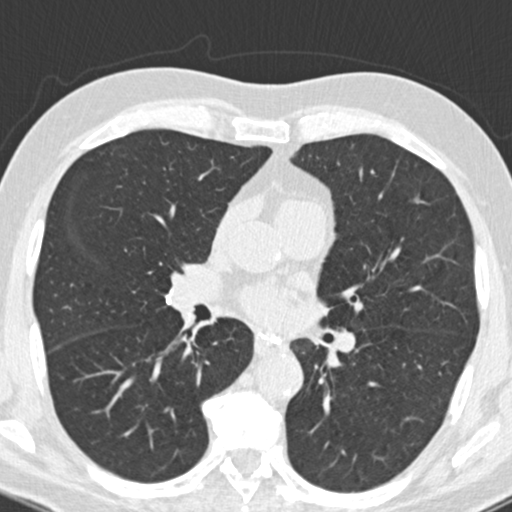
Chest CT (low-dose screening protocol), one axial image. Second screening round (one year after baseline). Lung window (W 1500 / L -600 HU). 2 mm slice thickness. Standard (soft-tissue) reconstruction kernel (B30f). 120 kVp. Slice 86 of 177 in the series. 512 × 512 image matrix, field of view 310 × 310 mm. Male, age 66 years at enrolment. Current smoker at enrolment.
Expert-annotated lung lesion, bounding box (x1, y1, x2, y2) in pixels: (182, 308, 210, 341). Reader record for this screening exam (exam-level; its link to the box is not recorded): non-calcified nodule or mass ≥4 mm, right upper lobe, 5 × 4 mm, smooth margins, pre-existing on the prior screen: yes; interval growth: no. Official screen result: positive, other. Participant outcome: lung cancer diagnosed 403 days after this screen (after the third annual screen) — squamous cell carcinoma, NOS, right lower lobe, poorly differentiated (G3), stage IIA (AJCC 6th edition), 22 mm at pathology.